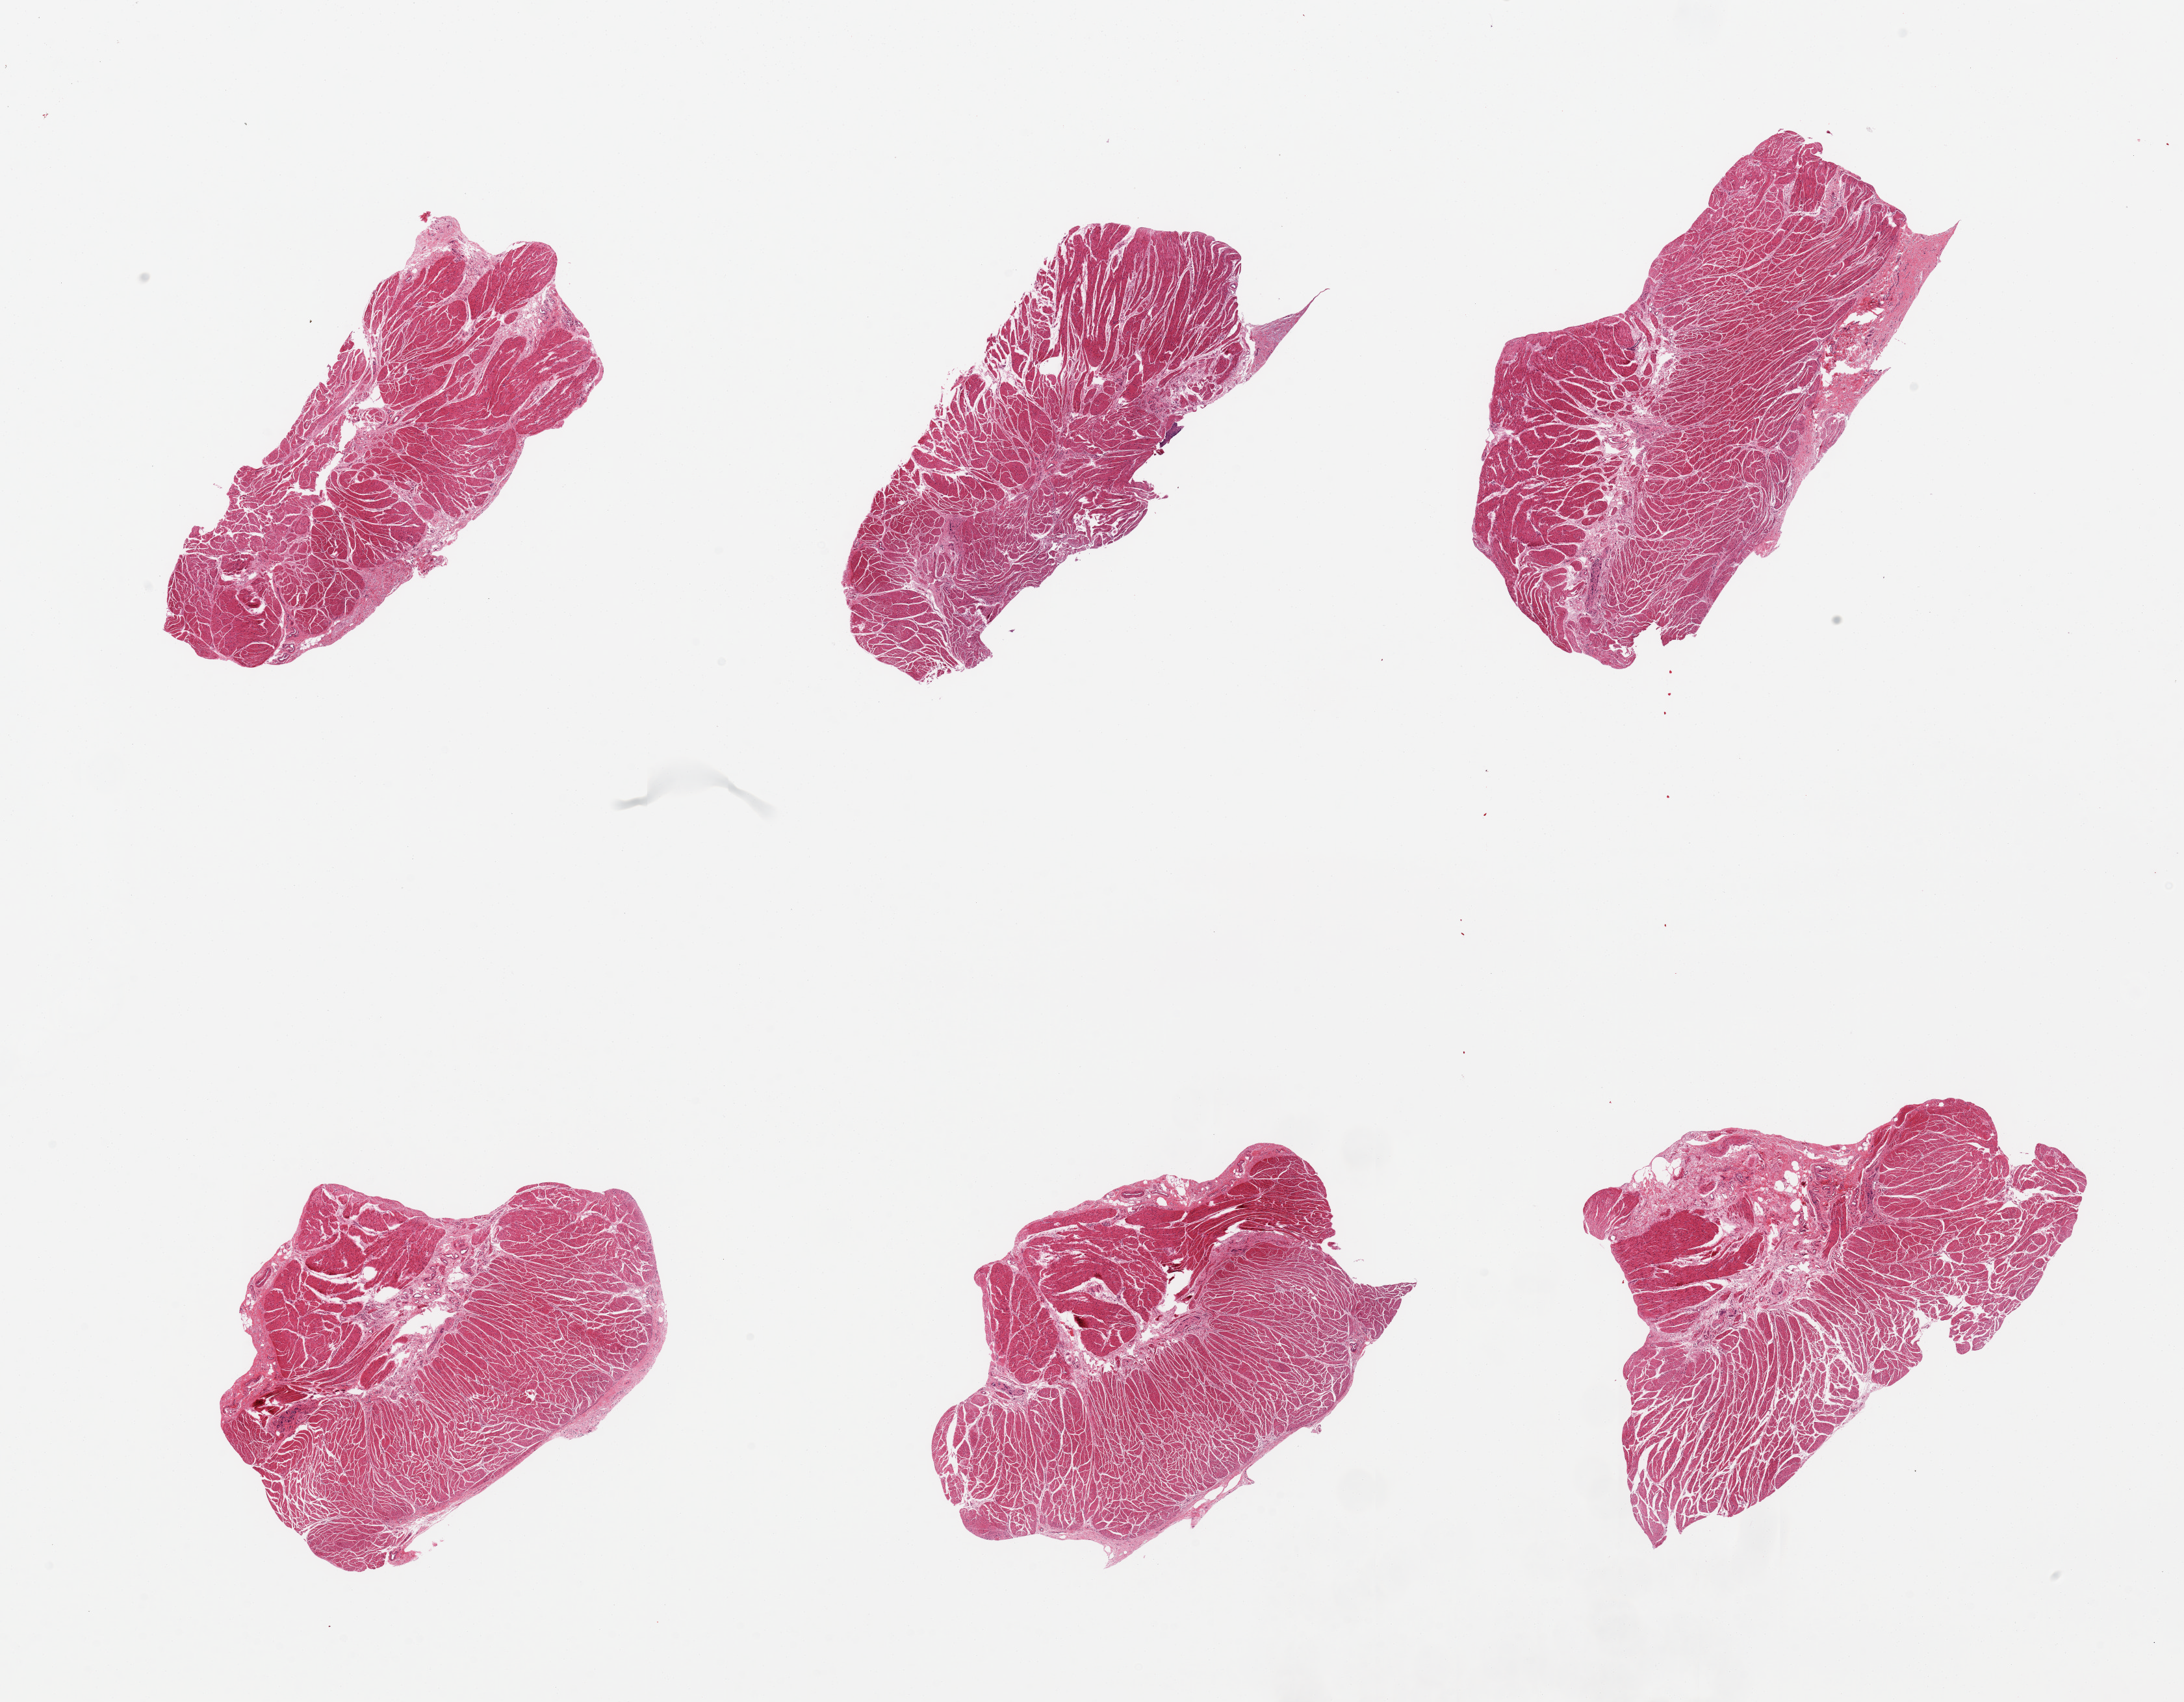
Hematoxylin and eosin (H&E) whole-slide image — whole scanned area (about 26.6 x 20.7 mm) shown as a low-resolution overview. PAXgene-fixed, paraffin-embedded tissue. Section of gastroesophageal junction (target tissue). Tissue donor sample. Donor: female.
Review note (as recorded): 6 pieces, all muscularis.